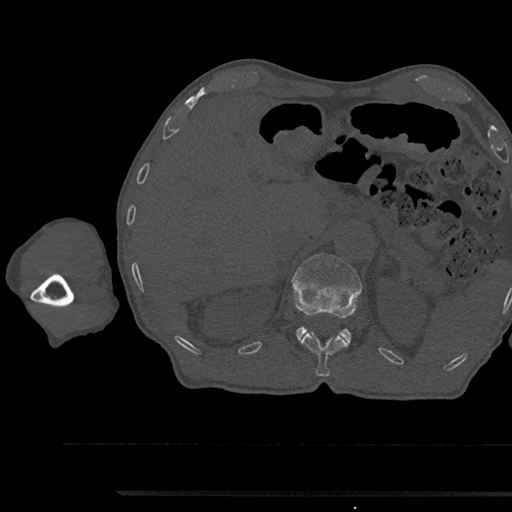
CT including the spine, one axial slice. Bone window (W 1800 / L 400 HU). 0.5 mm slice thickness. 512 × 512 image matrix, field of view 367 × 367 mm. Male patient, age 79 years. Case-level facts recorded for this patient, not image findings: primary cancer: prostate.
Annotated regions visible in this slice (semi-automatically segmented with operator editing):
- L1 vertebra: bounding box [x1, y1, x2, y2] px = [292, 254, 362, 342]
- T12 vertebra: [300, 332, 349, 377]